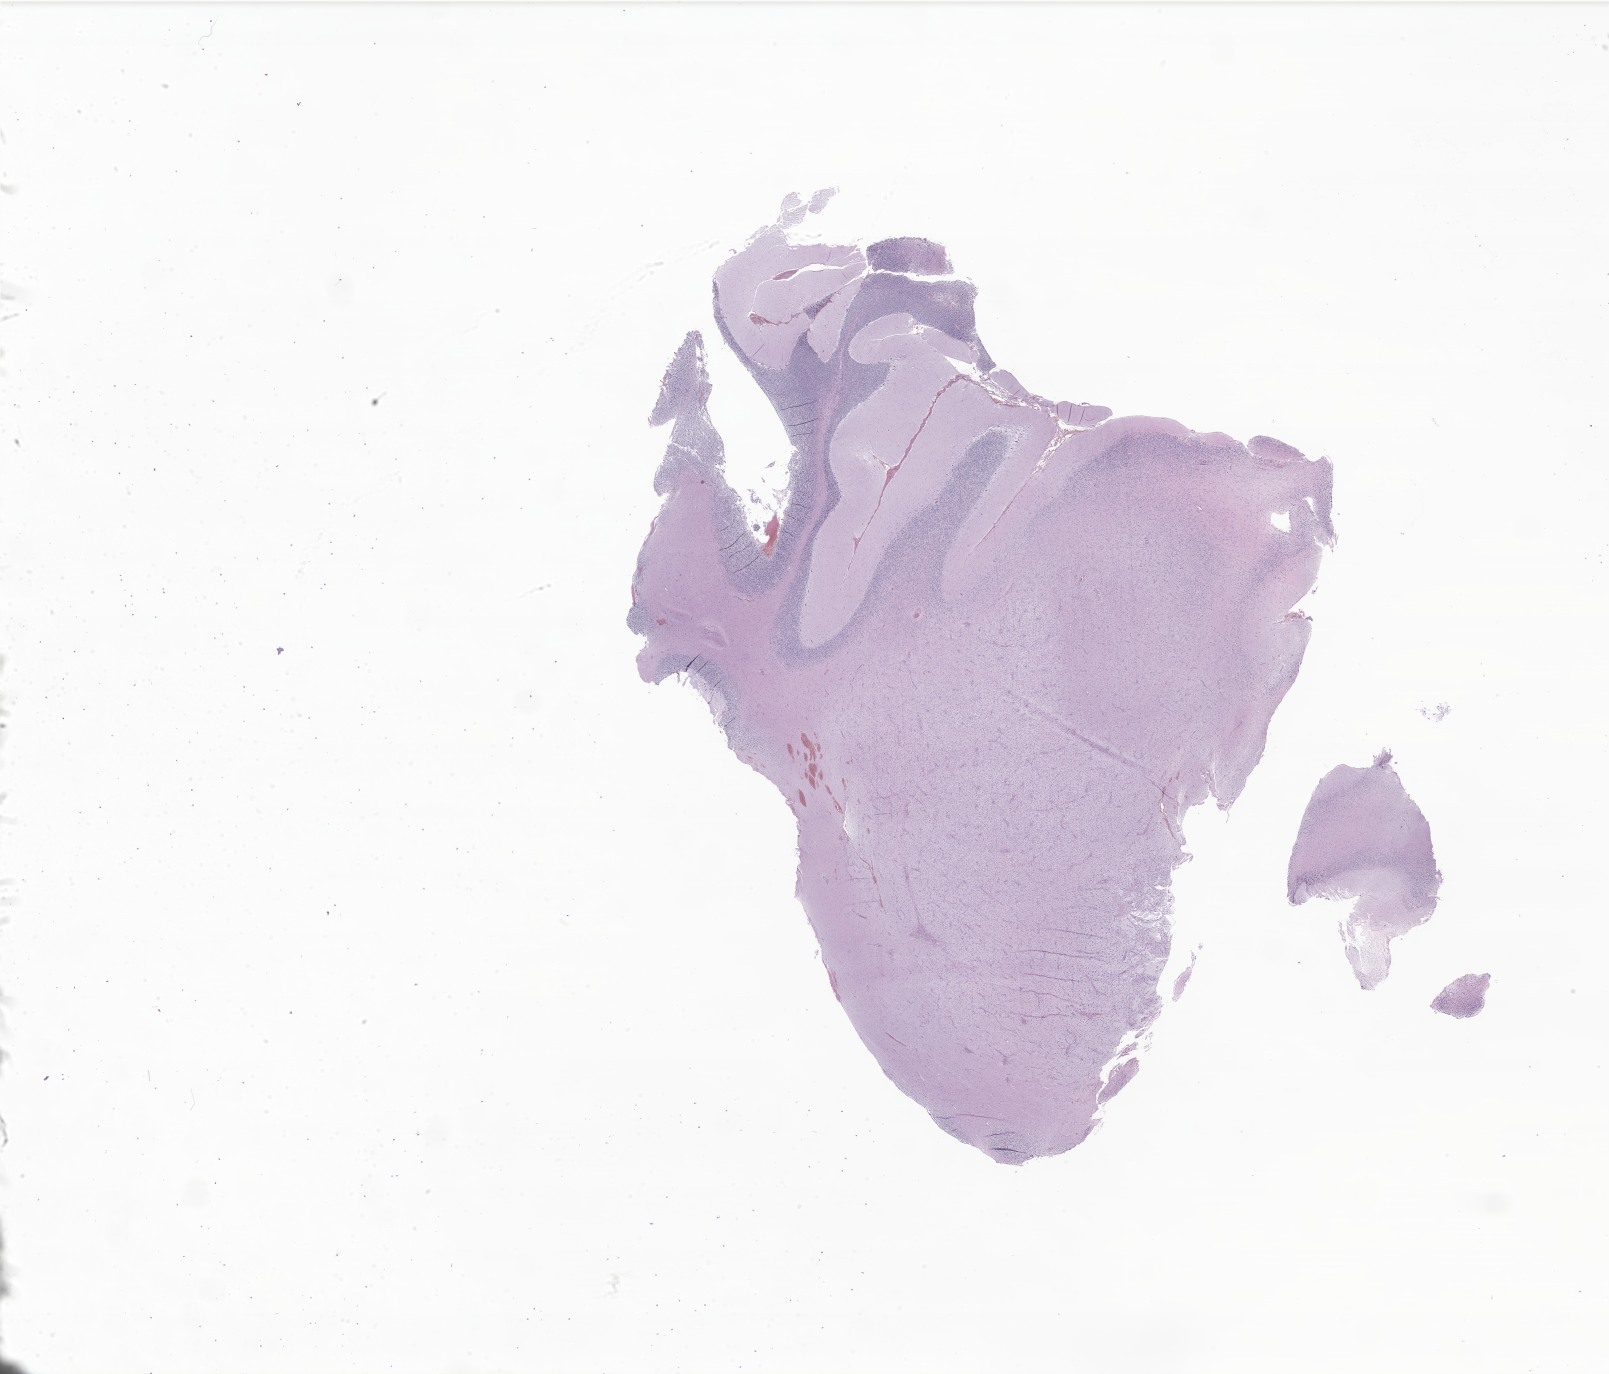
Whole-slide image, H&E stain of tumor tissue from the cerebellum, a low-resolution overview of the entire scanned area, about 27.1 x 23.2 mm; FFPE section. Patient: female, age 108 months.
Diagnosis (ICD-O-3 morphology term): Oligoastrocytoma, NOS.